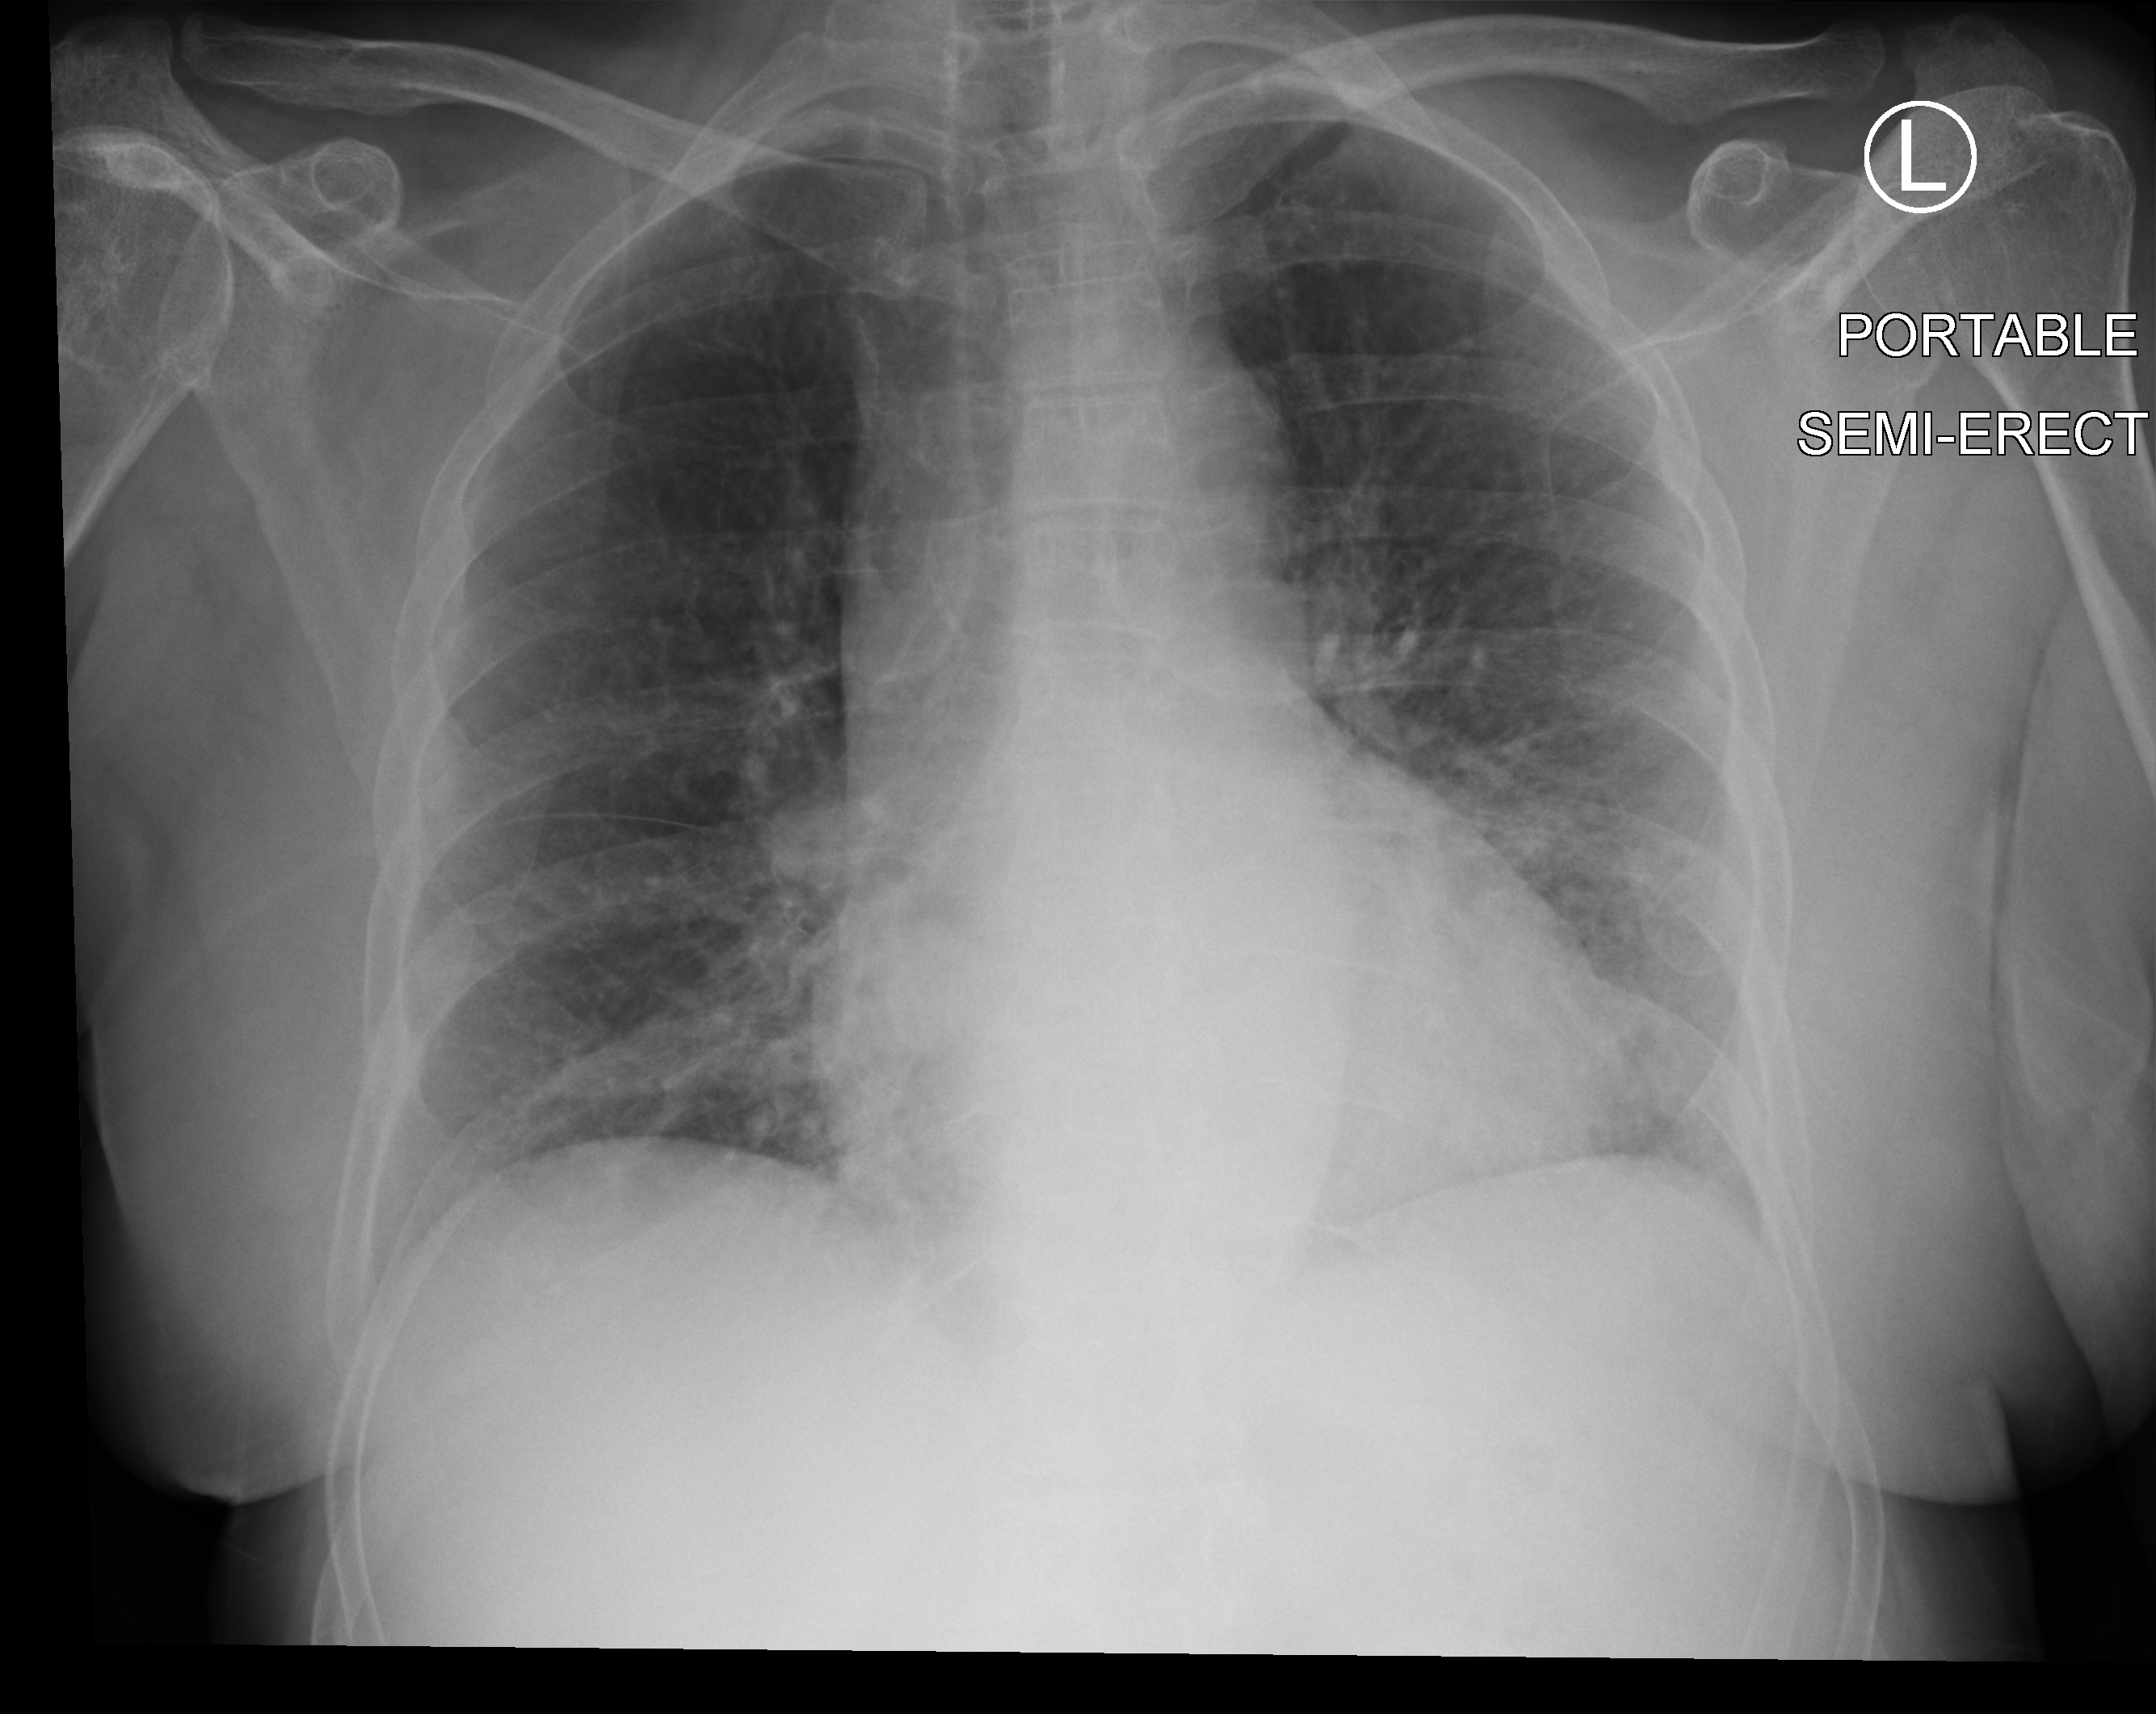
Chest X-ray (portable). Female patient hospitalised with COVID-19, age 60–74 years.
From the hospital-stay record, not from the radiograph (when in the stay this image was taken is not recorded): admitted to intensive care during this hospital stay: no.